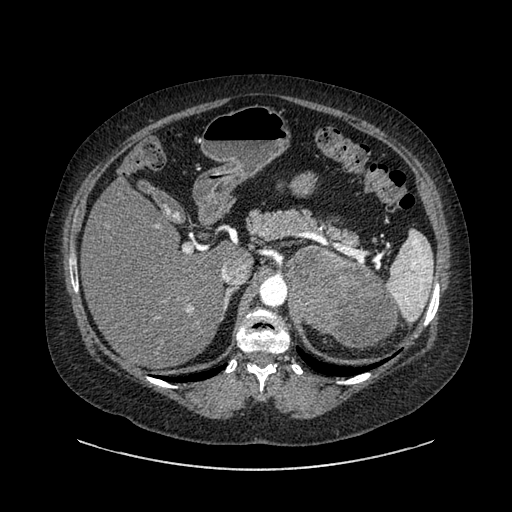
Contrast-enhanced abdominal CT, one axial slice; slice 592 of 769 in the series (ordered by position); reconstruction kernel SOFT; intravenous contrast given; soft-tissue window (W 400 / L 40 HU); 0.62 mm slice thickness; 512 × 512 image matrix, field of view 460 × 460 mm. Female patient, age 61 years. Case-level facts recorded for this patient, not image findings: diagnosis: adrenocortical carcinoma; tumour side: left adrenal; tumour size at pathology: 13 cm.
Outlined on this slice (semi-automatic segmentation, software-assisted and operator-edited):
- mass: bounding box [x1, y1, x2, y2] px = [287, 249, 394, 346]